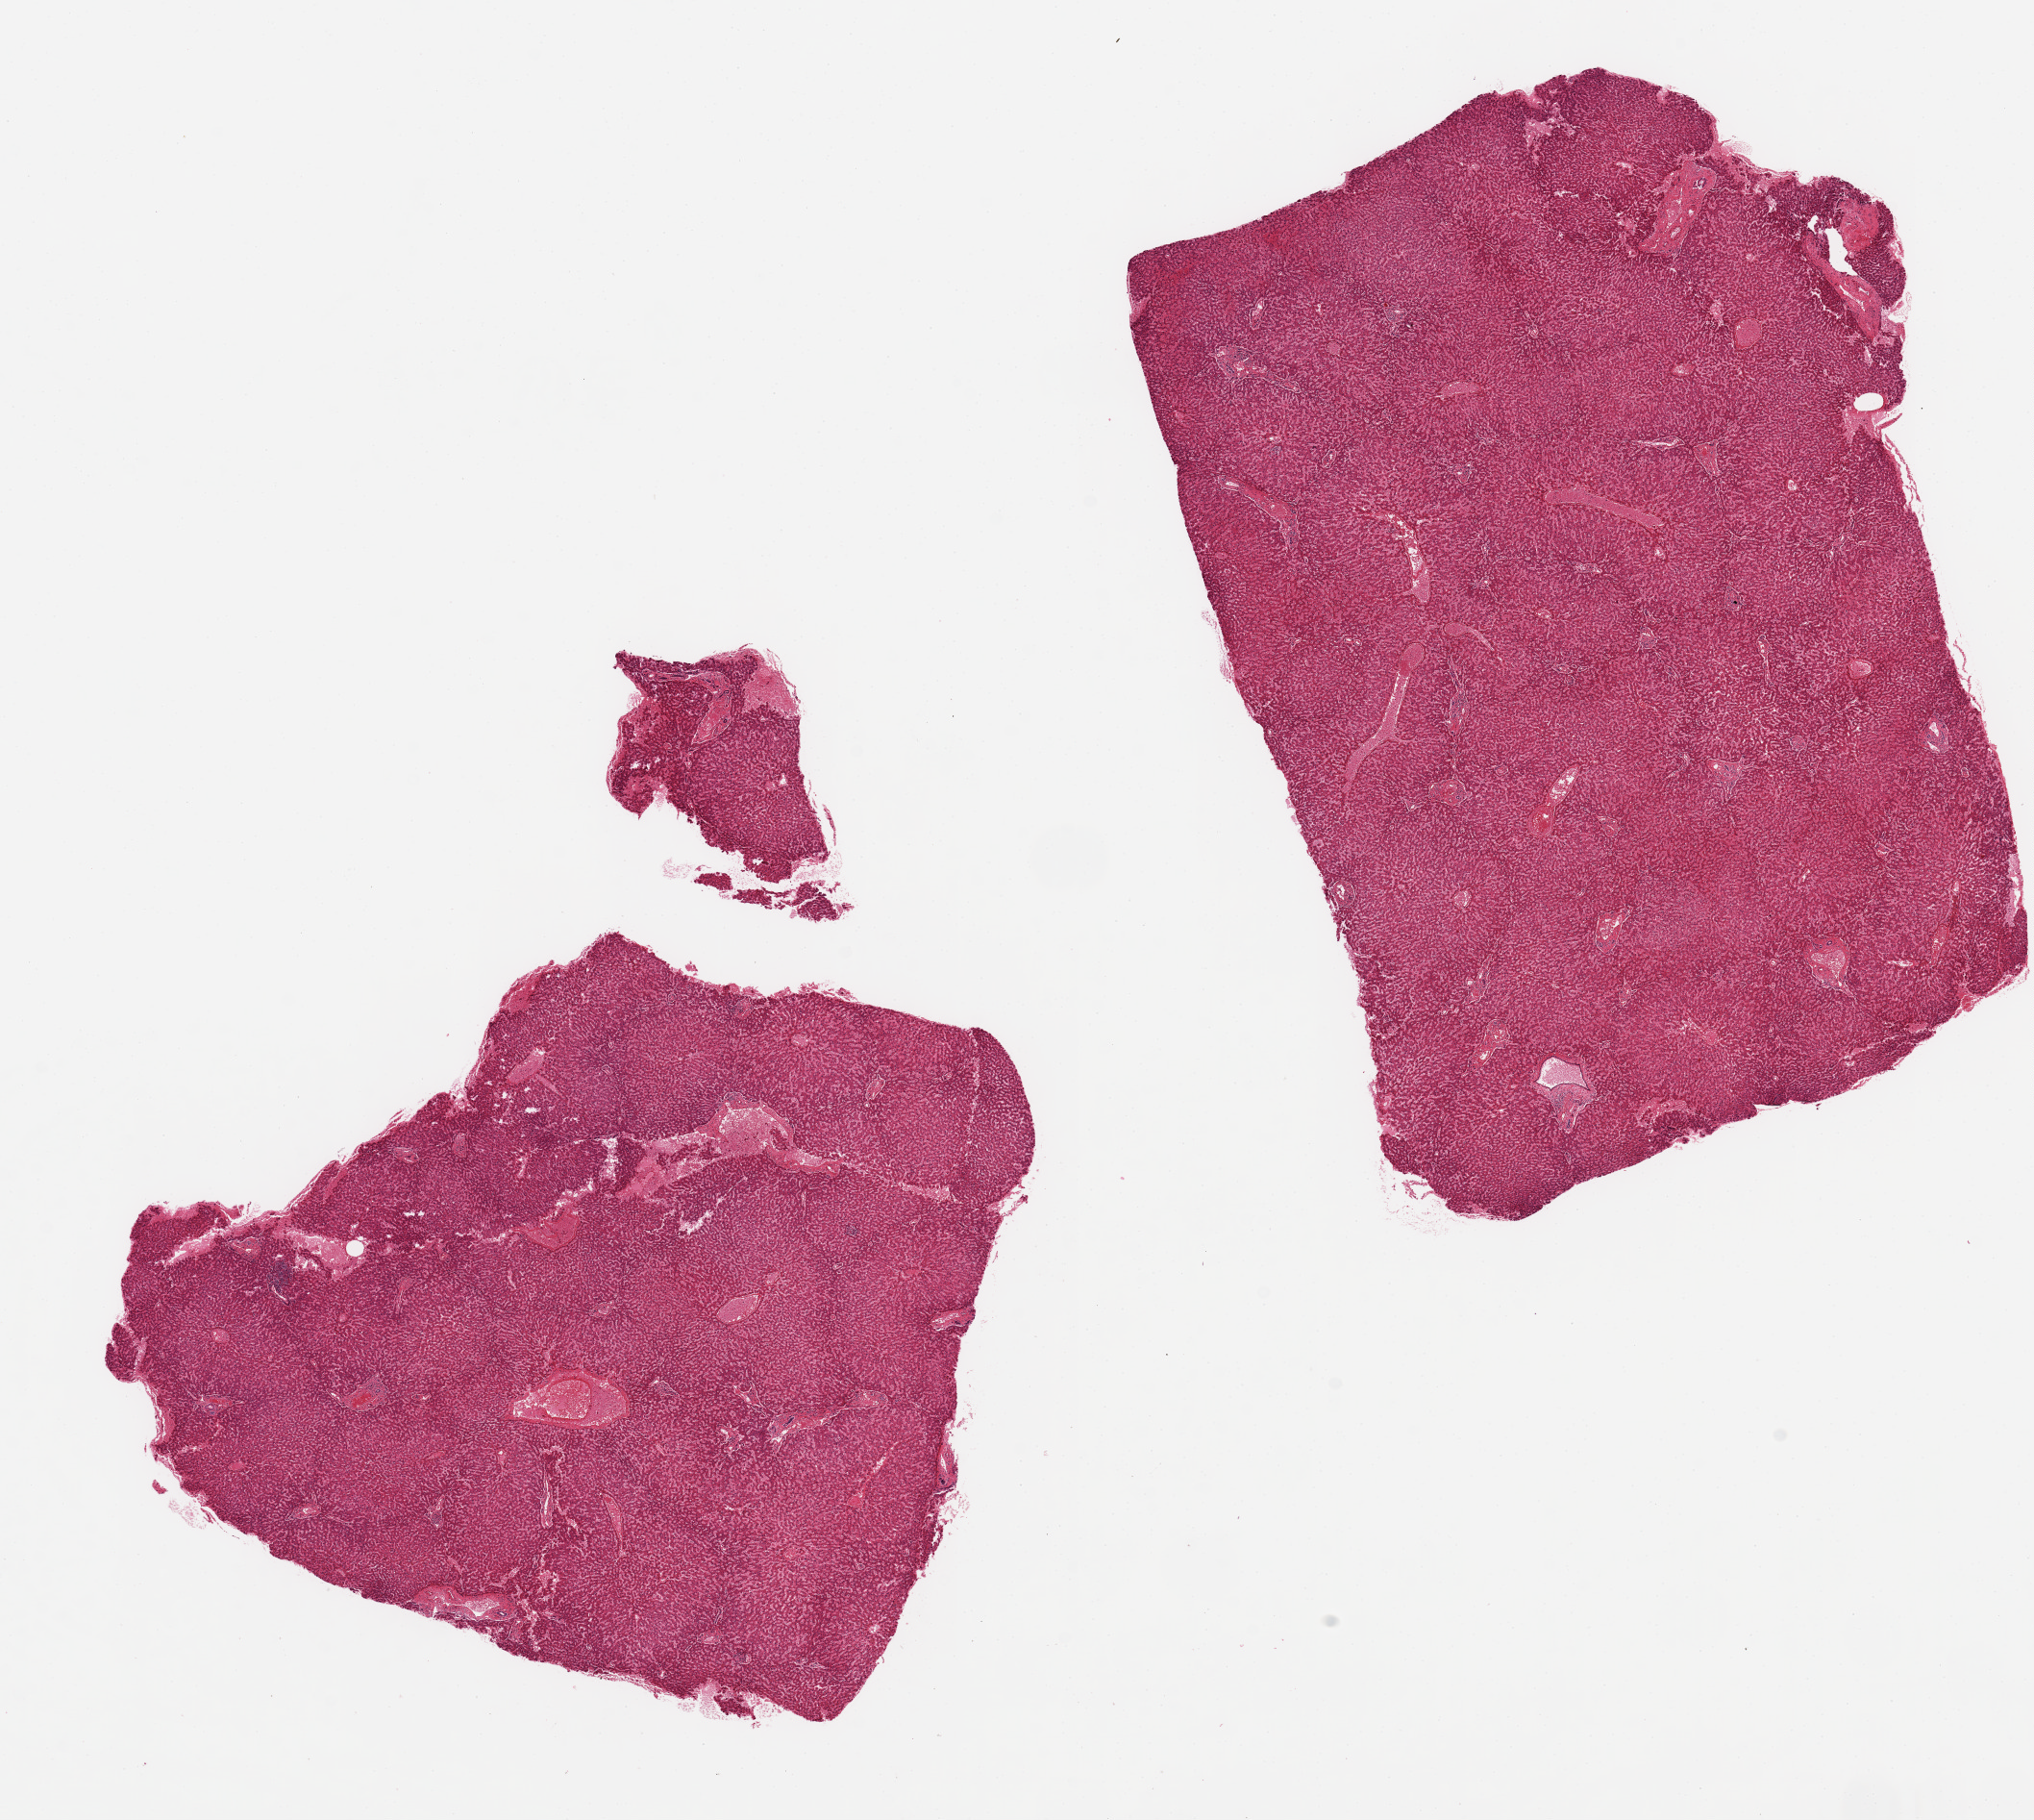
Whole-slide image, H&E stain, low-resolution overview of the scanned area, about 16.7 x 15.0 mm; PAXgene-fixed paraffin-embedded (PFPE) section; target tissue: liver; tissue donor sample. Male donor.
Pathologist's review note for this sample: 2 aliquots, ~8x6mm, moderate congestion.